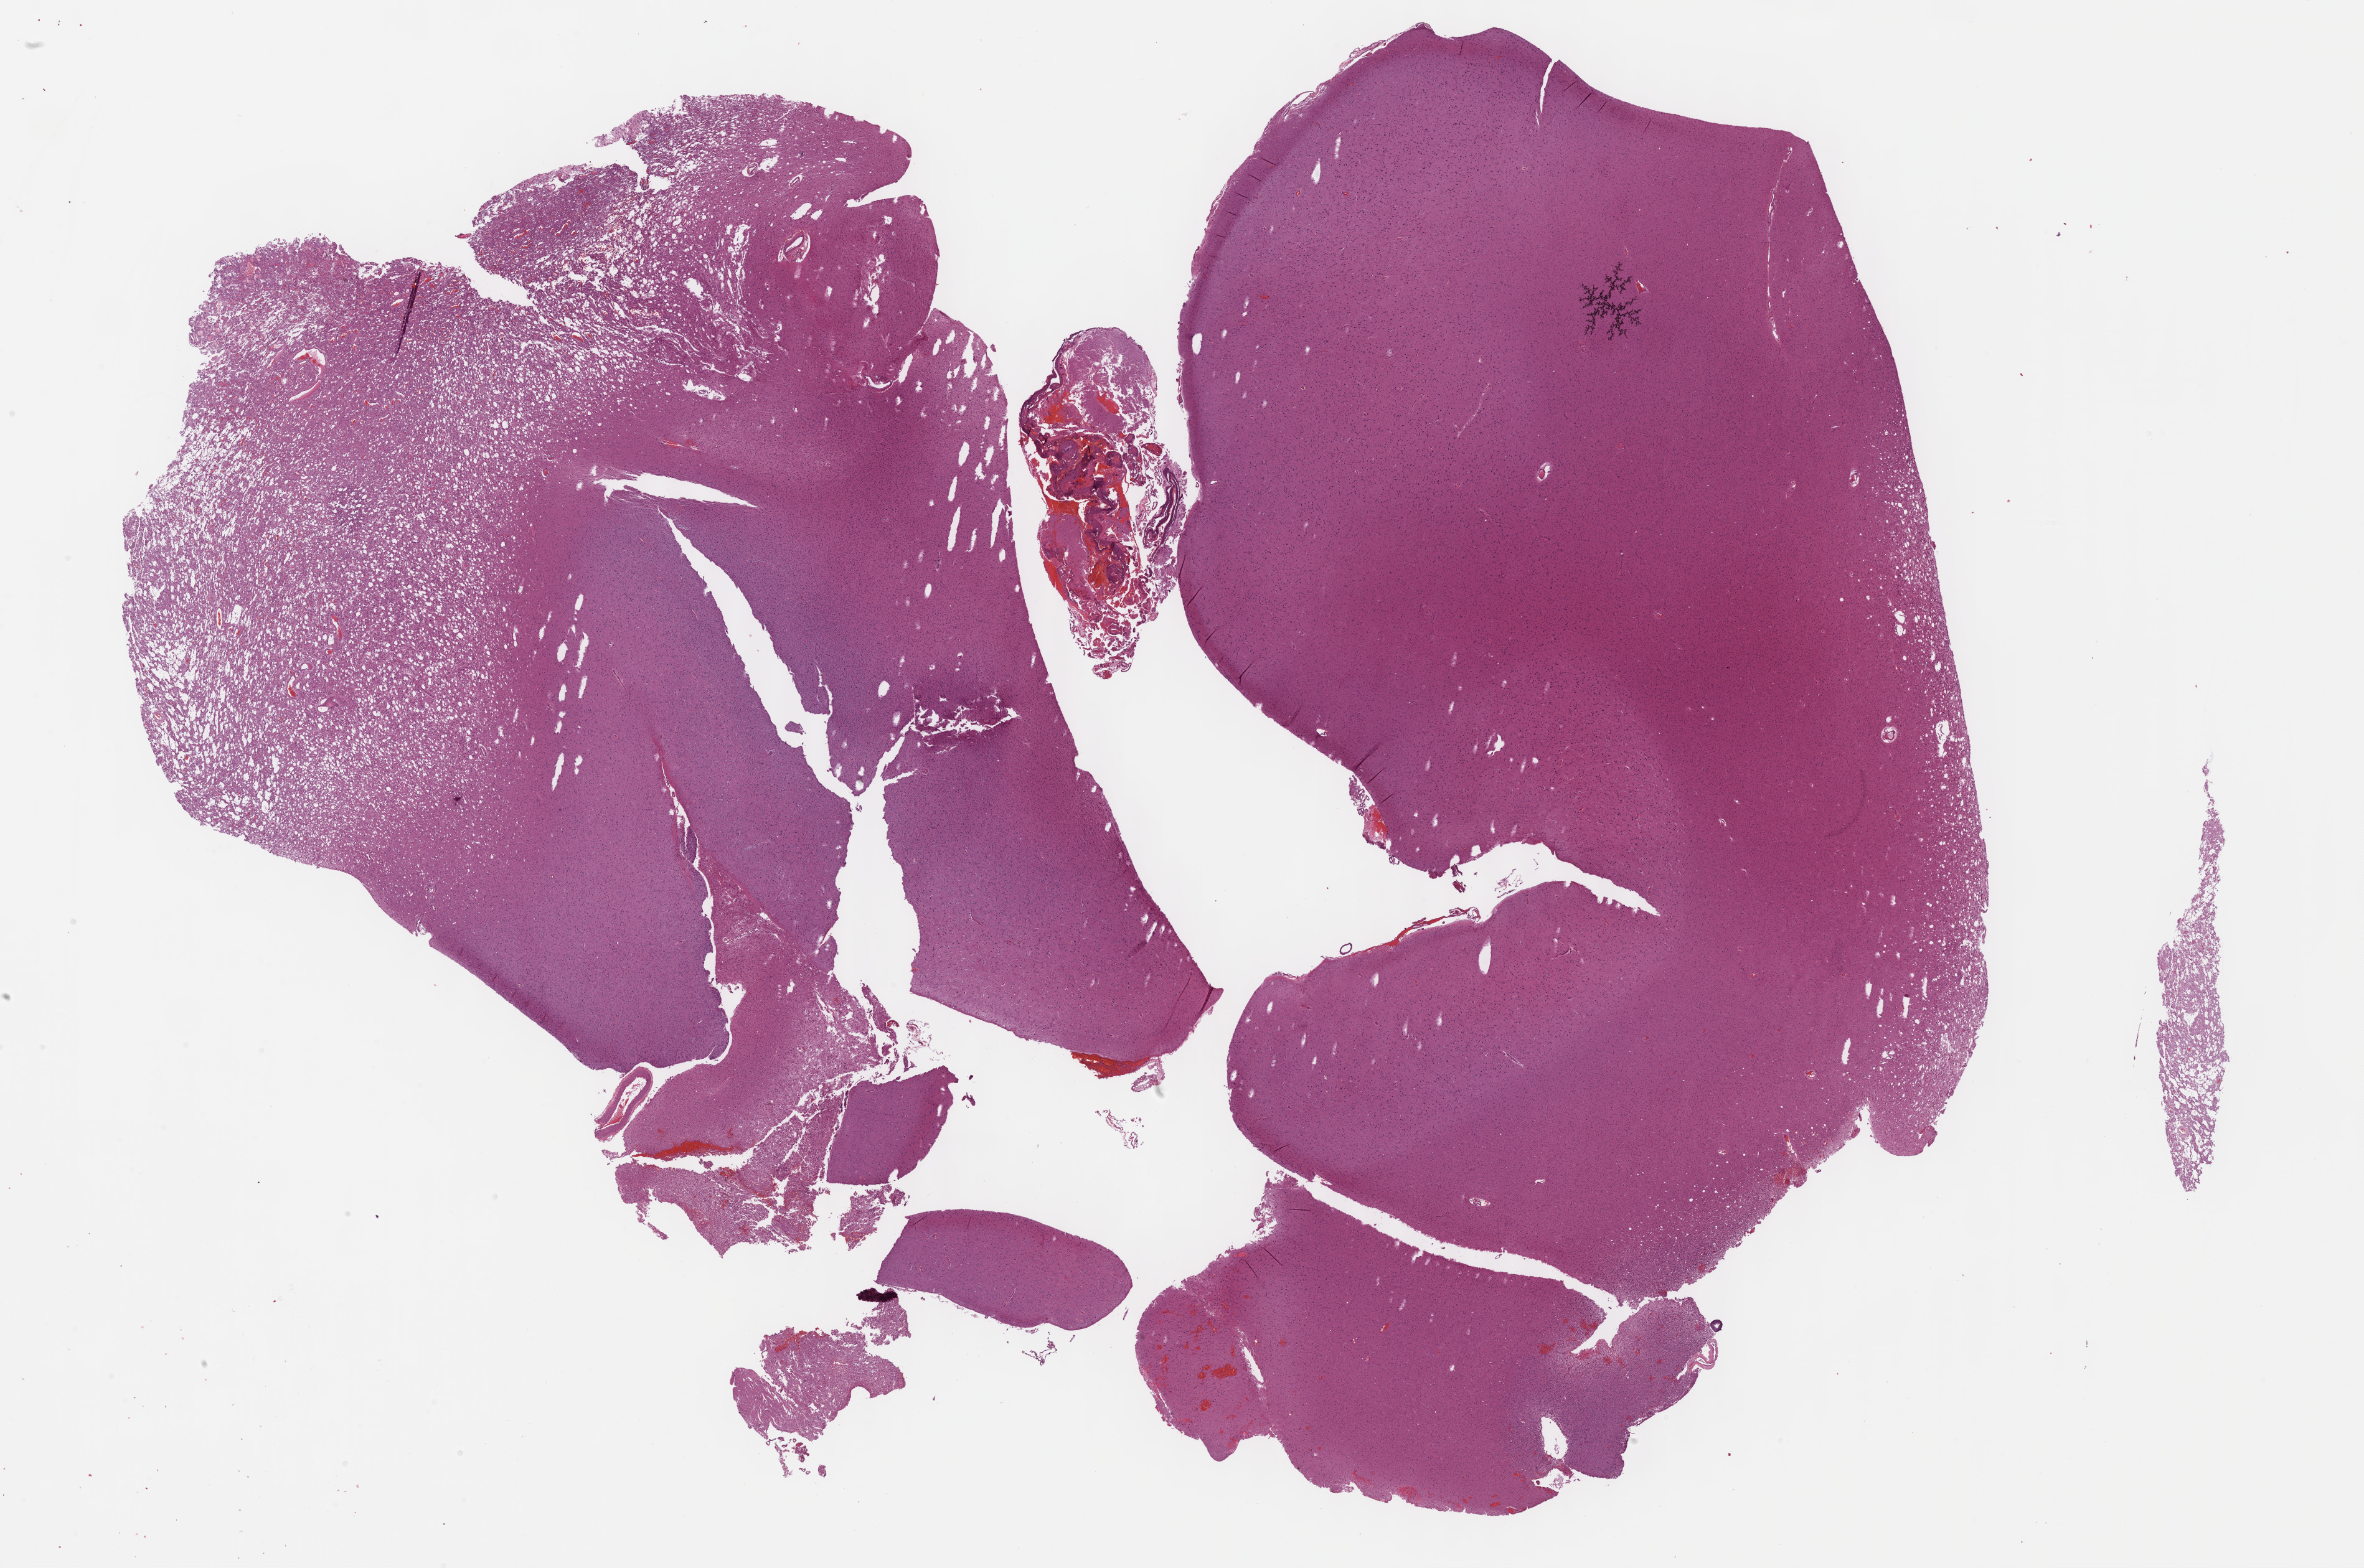
Whole-slide histology image, H&E-stained — whole scanned area (about 30.7 x 20.4 mm) shown as a low-resolution overview. FFPE section. Brain, primary tumour sample. Male patient; age at initial diagnosis 61 years.
Pathologic diagnosis: Mixed glioma.